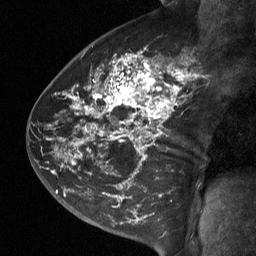
Breast MRI (dynamic contrast-enhanced), one sagittal slice. Position 41 of 64 along the scan axis. Dynamic contrast-enhanced study with each time point stored as its own series, time point 2 of 3 at this slice position (early post-contrast, ordered by acquisition time). 1.5 T. TE 4.8 ms, TR 27 ms. 256 × 256 image matrix, field of view 200 × 200 mm. Patient: female, 42 years. From the clinical record (not read from this slice): setting: breast cancer imaged before/during neoadjuvant chemotherapy; receptor status: triple-negative.
Outlined on this slice (semi-automatically segmented with operator editing):
- analysis volume of interest (the breast-tissue region the enhancement analysis was run in; not a lesion): bounding box <49,45,198,197> (left, top, right, bottom; pixels)
- tumour enhancement mask (voxels above the 90 % enhancement threshold inside the analysis volume of interest): <72,55,187,164>